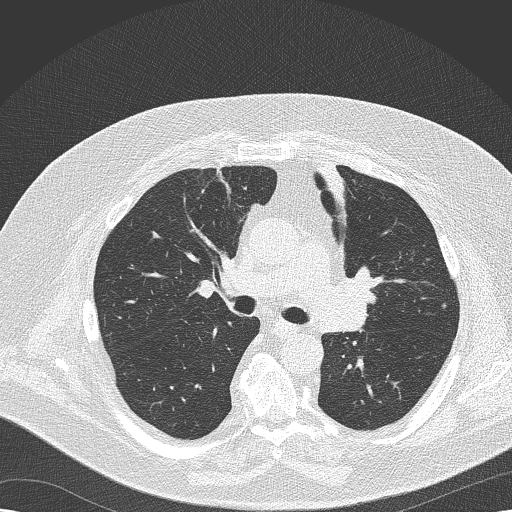
Axial slice from a low-dose chest CT screening exam; second annual screen; lung window (W 1500 / L -600 HU); 2 mm slice thickness; lung (sharp) reconstruction kernel (B50f); slice 70 of 173 in the series. Male, age 68 years at enrolment.
Lesion marked by an expert reader, bounding box [x1, y1, x2, y2] px = [321, 264, 382, 326]. Screening reader's record for this exam (one nodule recorded; not confirmed to be the boxed lesion): non-calcified nodule or mass ≥4 mm, left lower lobe, 8 × 6 mm, soft tissue attenuation, pre-existing on the prior screen: yes; interval growth: no. Later outcome: lung cancer diagnosed 256 days after this screen — squamous cell carcinoma, NOS, left upper lobe, poorly differentiated (G3), stage IIB (AJCC 6th edition), 35 mm at pathology.